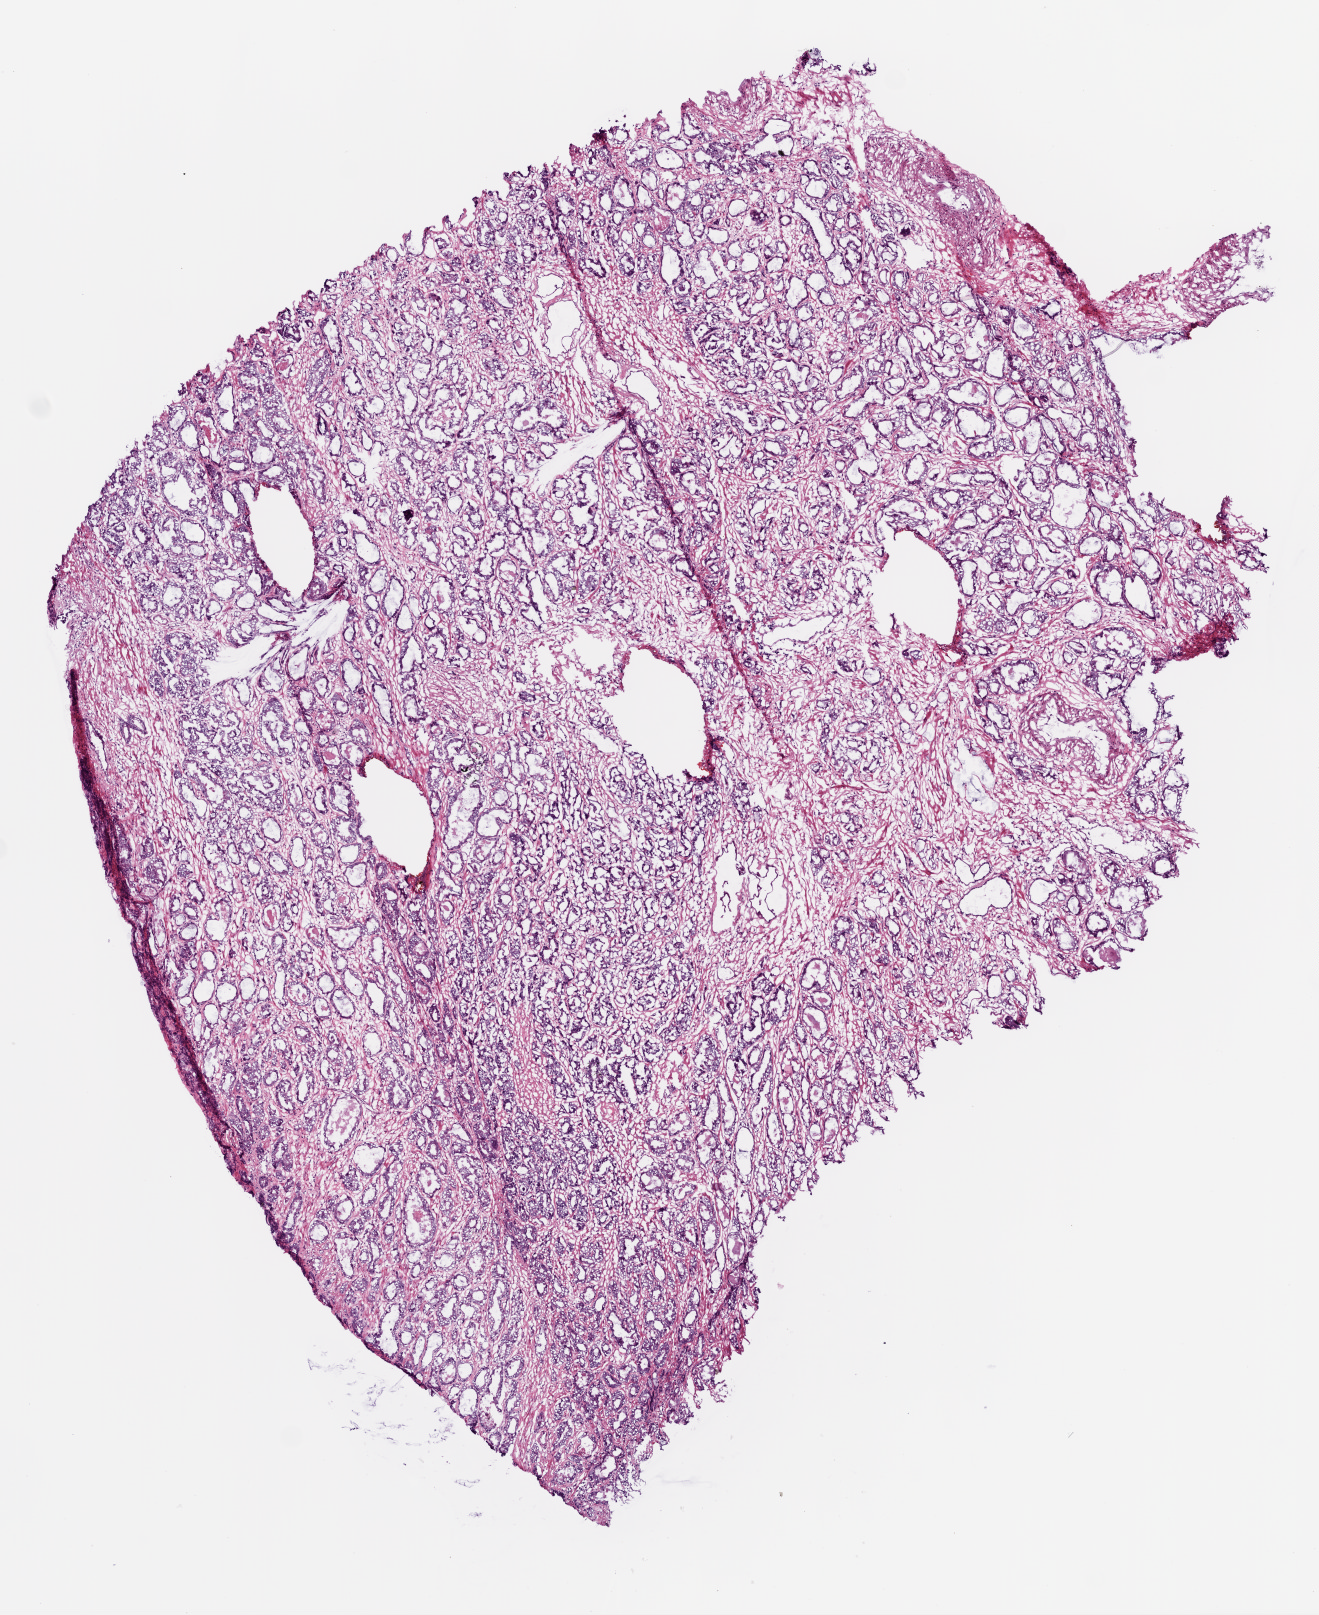
H&E-stained whole-slide image — a low-resolution overview of the entire scanned area, about 5.3 x 6.5 mm; frozen section; sample: primary tumour, prostate. Male patient; age at initial diagnosis 72 years. Gleason score: 7 (3+4). Composition of this section per pathologist review: tumour cells 80%, tumour nuclei 80%, normal cells 10%, stromal cells 10%, necrosis 0%.
Histologic diagnosis: Acinar cell carcinoma (prostate gland). Laterality: bilateral.